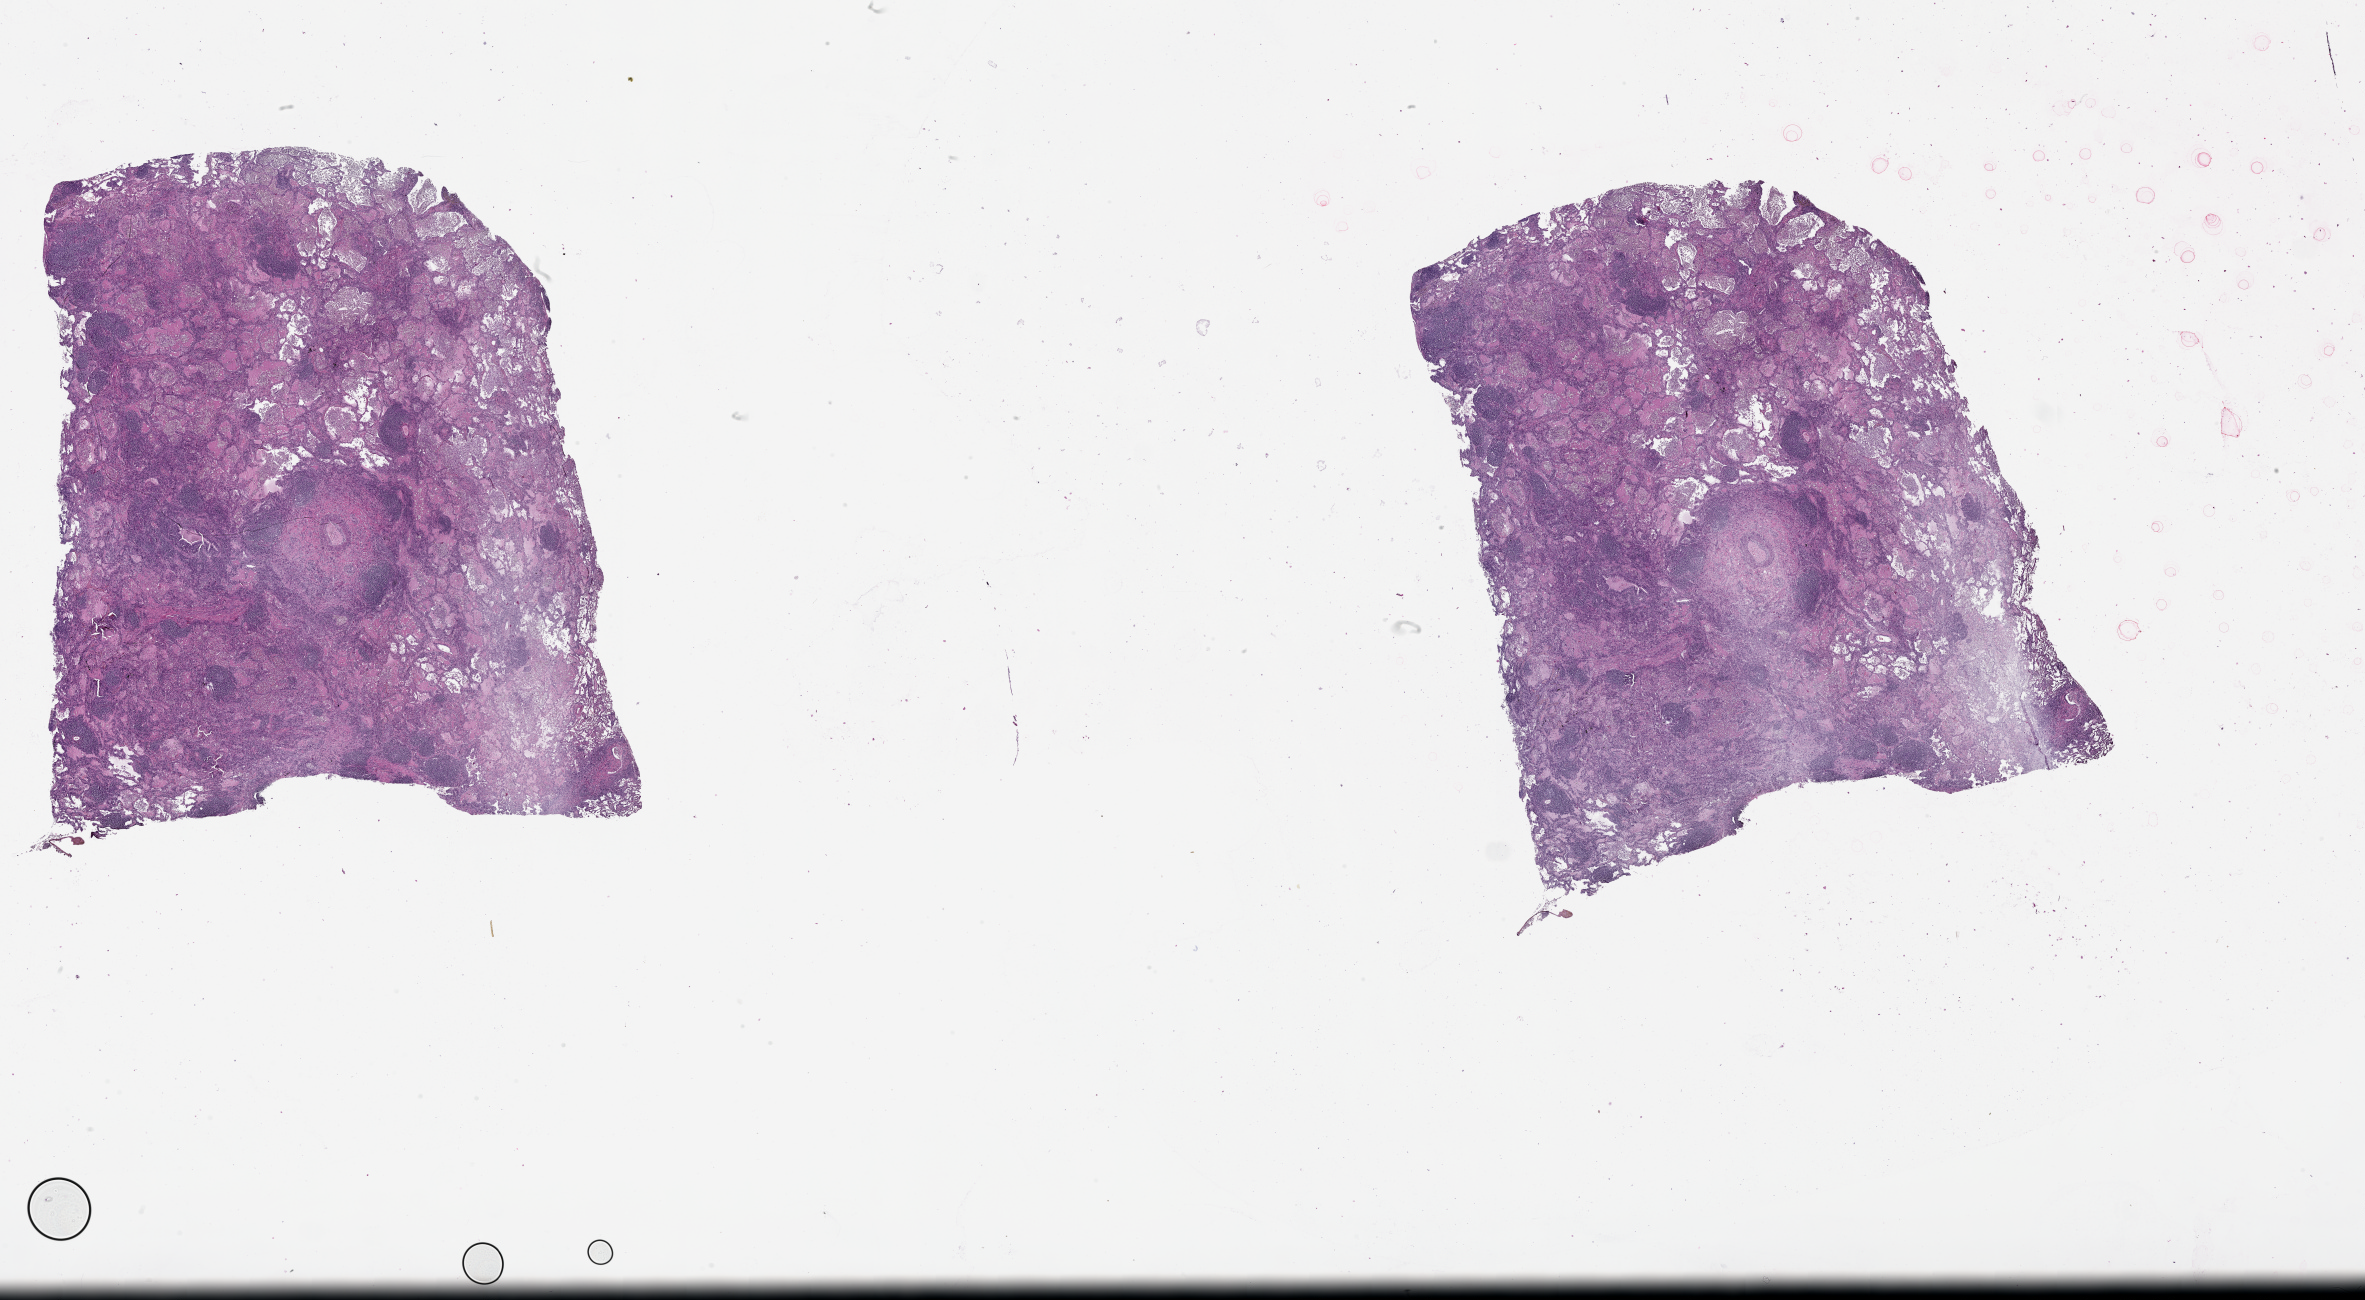
Digitized H&E-stained tissue section (whole slide) — a low-resolution overview of the entire scanned area, about 38.1 x 20.9 mm. Lung, tumour tissue. Female, 58 y/o.
Patient diagnosis (cohort enrolment): squamous cell carcinoma (lung).